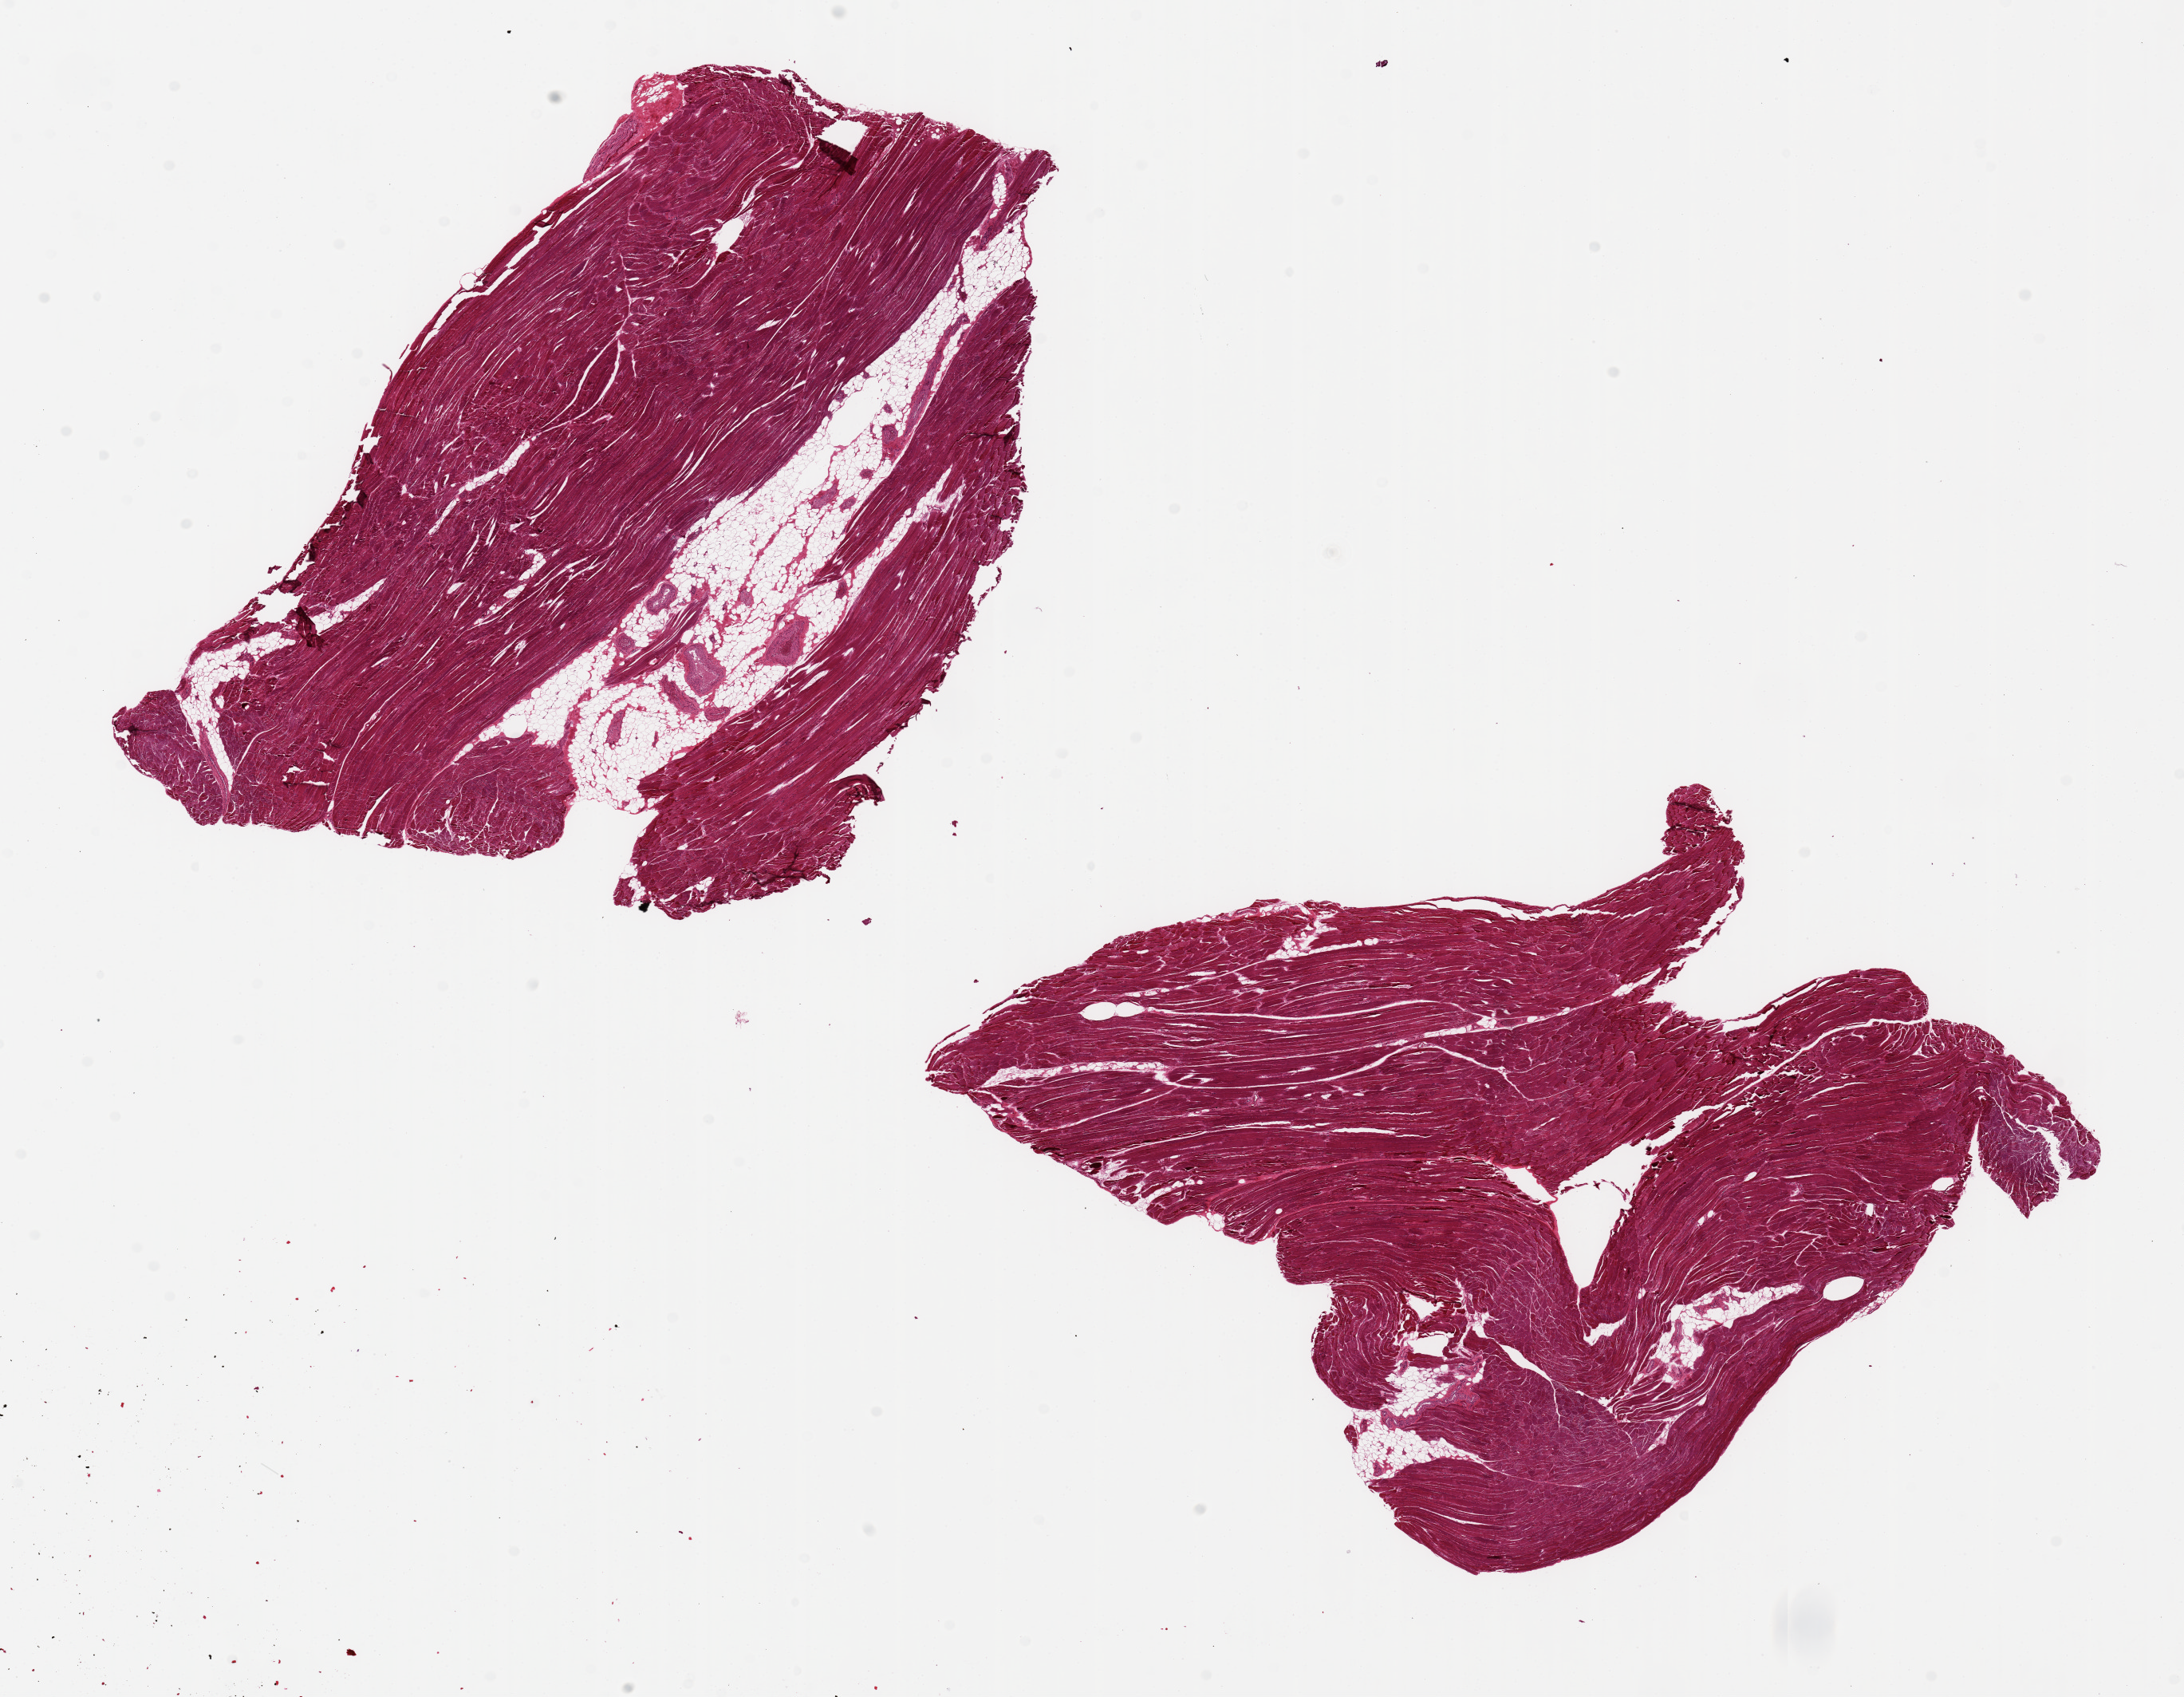
Whole-slide image, haematoxylin and eosin stain, a low-resolution overview of the entire scanned area, about 21.7 x 16.8 mm (slide scanned at 20x). Donor sex: male.
Specimen: PAXgene-fixed, paraffin-embedded tissue; section of skeletal muscle (target tissue); donor tissue sample.